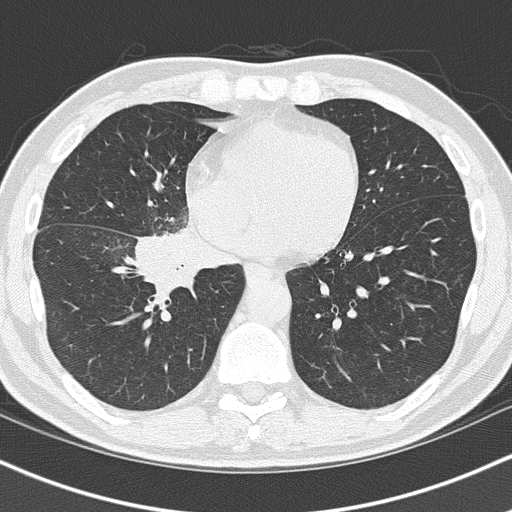
Chest CT (low-dose screening protocol), one axial image, first (baseline) screen, lung window (W 1500 / L -600 HU), 2 mm slice thickness, lung (sharp) reconstruction kernel (B50f), 120 kVp, slice 49 of 151 in the series. Male, age 55 years at enrolment. Current smoker at enrolment.
- Expert reader's lesion annotation, bounding box (x1, y1, x2, y2) in pixels: (128, 225, 240, 310).
- Screening reader's record for this exam (one nodule recorded; not confirmed to be the boxed lesion): non-calcified nodule or mass ≥4 mm, right lower lobe, 6 × 5 mm, spiculated (stellate) margins, soft tissue attenuation.
- Official screen result: positive, change unspecified: nodule(s) >= 4 mm or enlarging nodule(s), mass(es), or other non-specific abnormalities suspicious for lung cancer.
- Lung cancer was diagnosed 21 days after this screen: carcinoma, NOS, right hilum, stage IB (AJCC 6th edition), 67 mm at pathology.